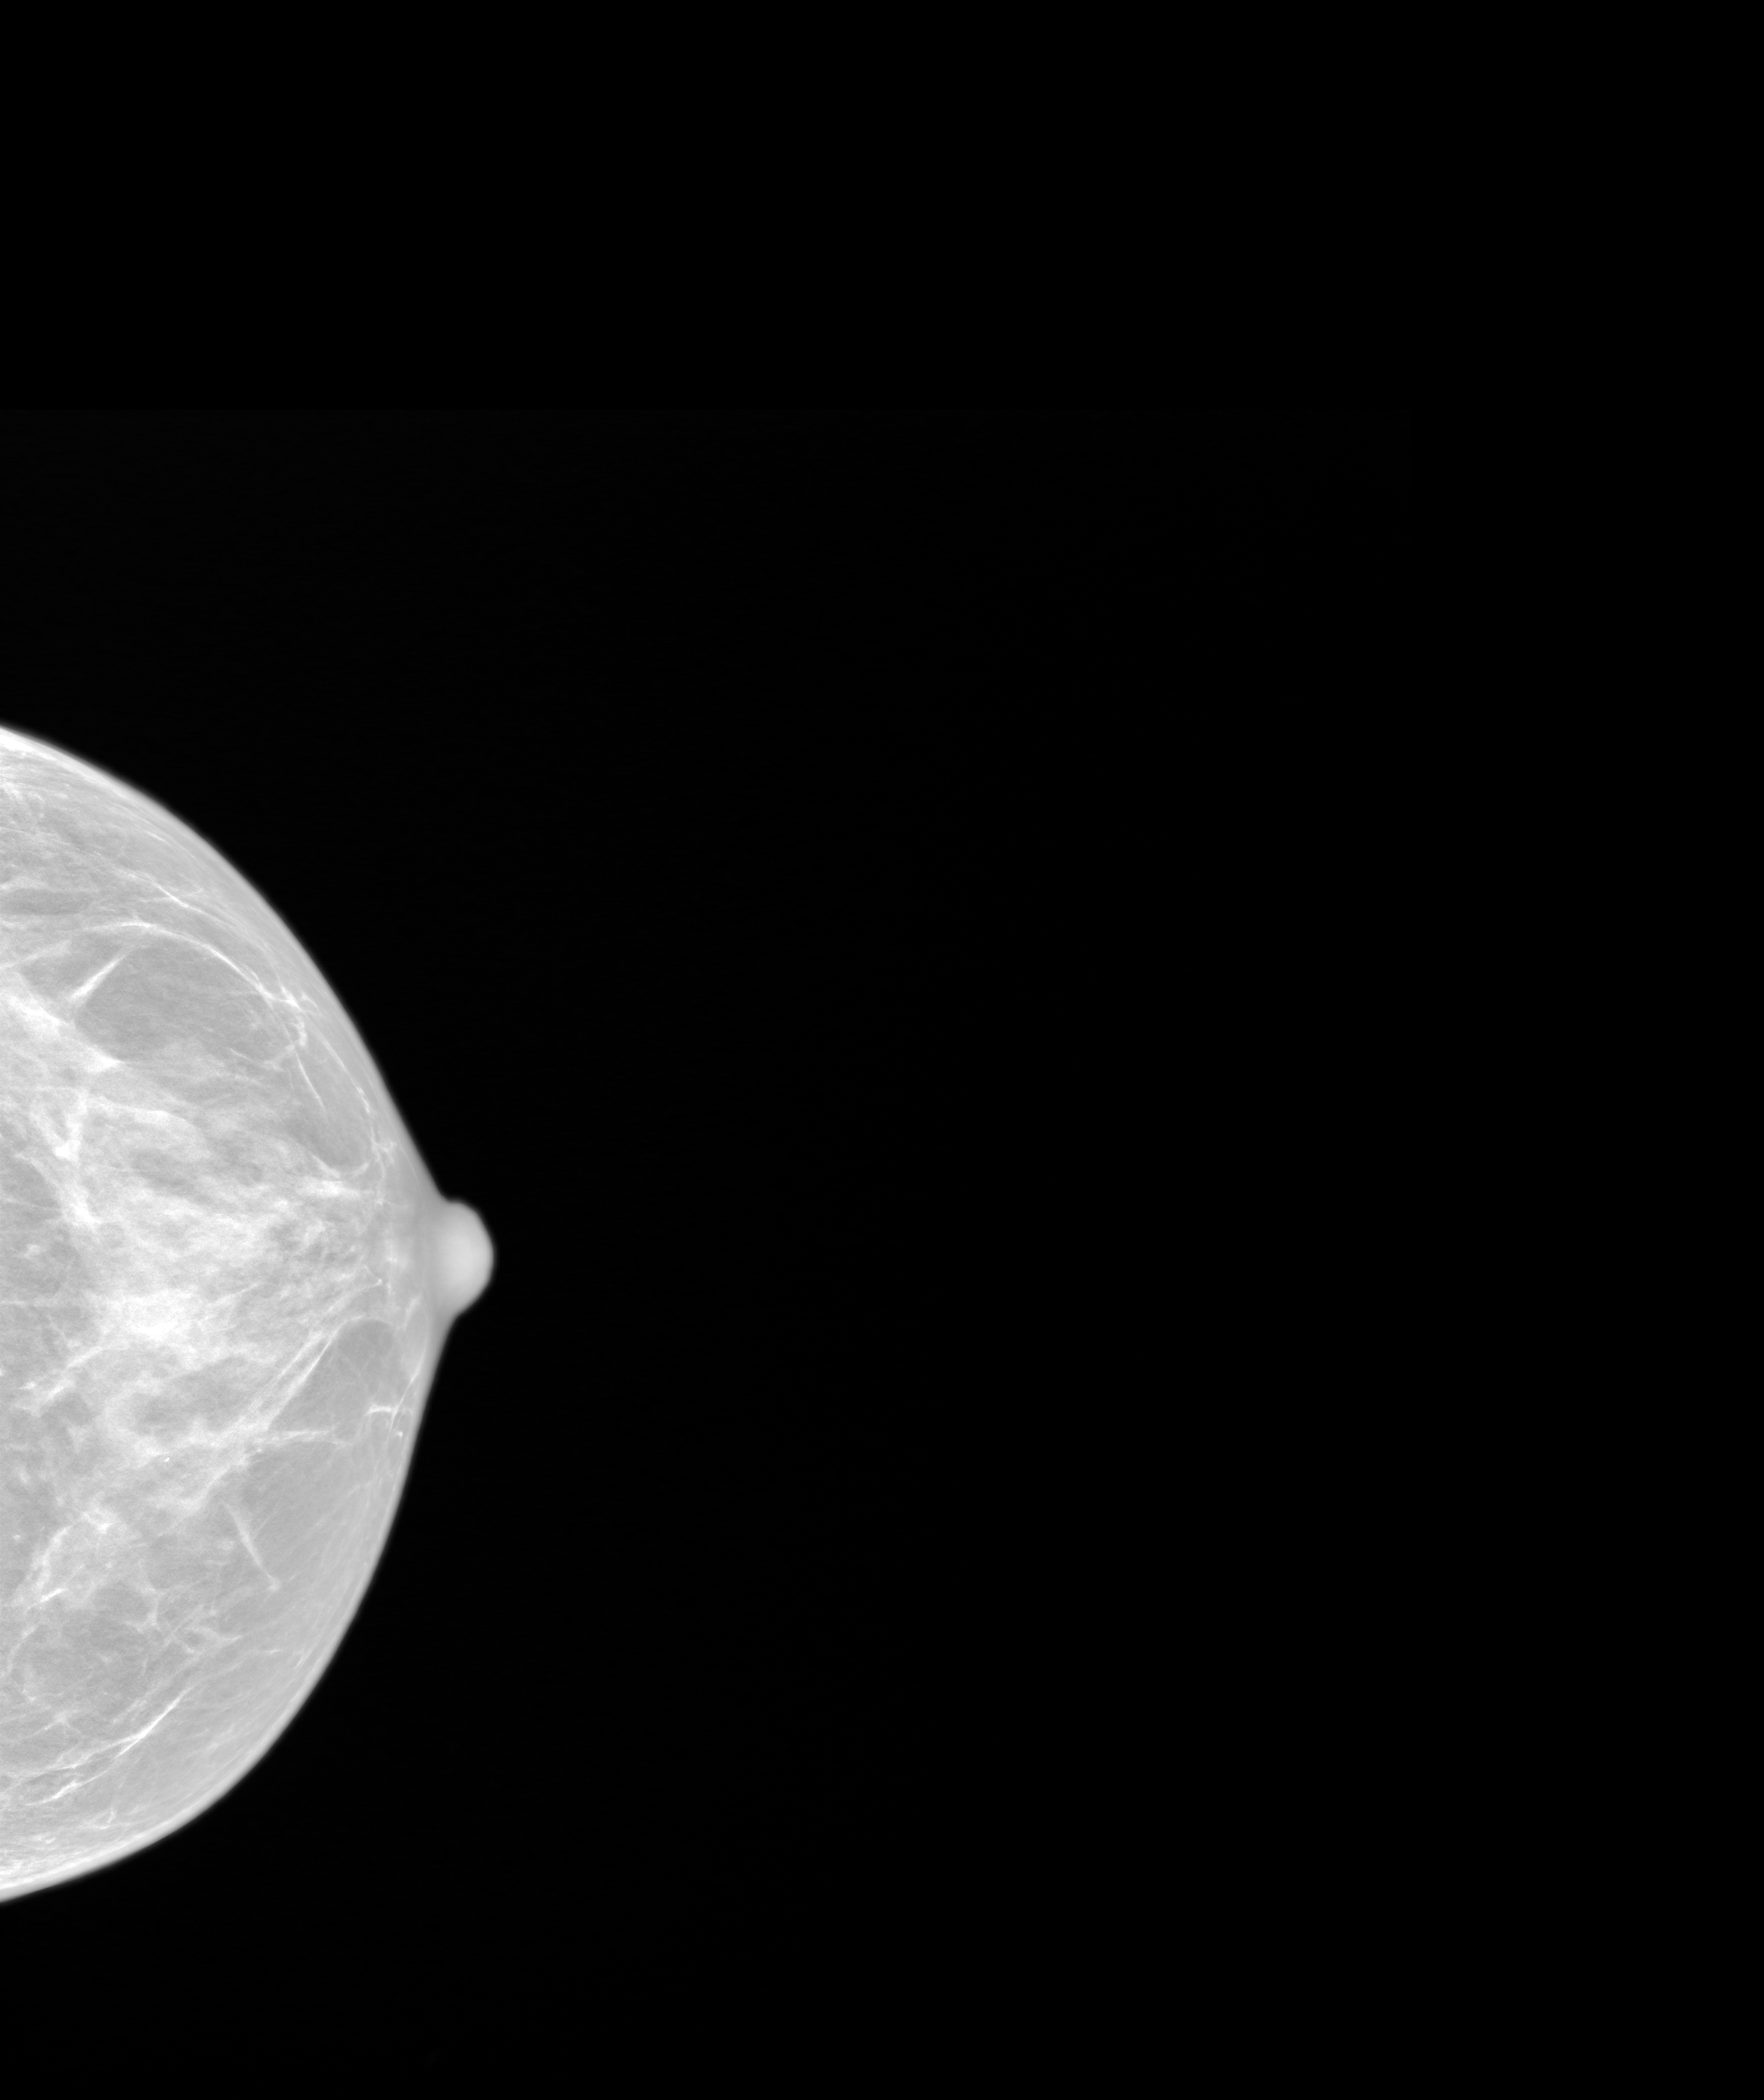
Screening examination. Patient aged 65 years (female).
Image type: synthesized 2-D view from tomosynthesis. Breast: left. Projection: cranio-caudal projection.